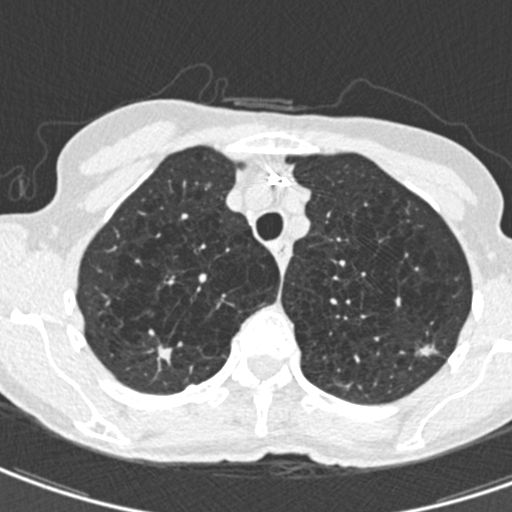
Chest CT (low-dose screening protocol), one axial image. Second annual screen. Lung window (W 1500 / L -600 HU). 0.75 mm slice thickness. 512 × 512 image matrix, field of view 272 × 272 mm. Female, age 71 years at enrolment. Current smoker at enrolment.
- Expert reader's lesion annotation, box from (x=404, y=332) to (x=444, y=370) px.
- The screening reader recorded 2 non-calcified nodules or masses ≥4 mm on this exam (right upper lobe, left upper lobe); which of them this box marks is not recorded.
- Later outcome: lung cancer diagnosed 604 days after this screen (after the third annual screen) — adenocarcinoma, NOS, left upper lobe, moderately differentiated (G2), stage IA (AJCC 6th edition), 12 mm at pathology.